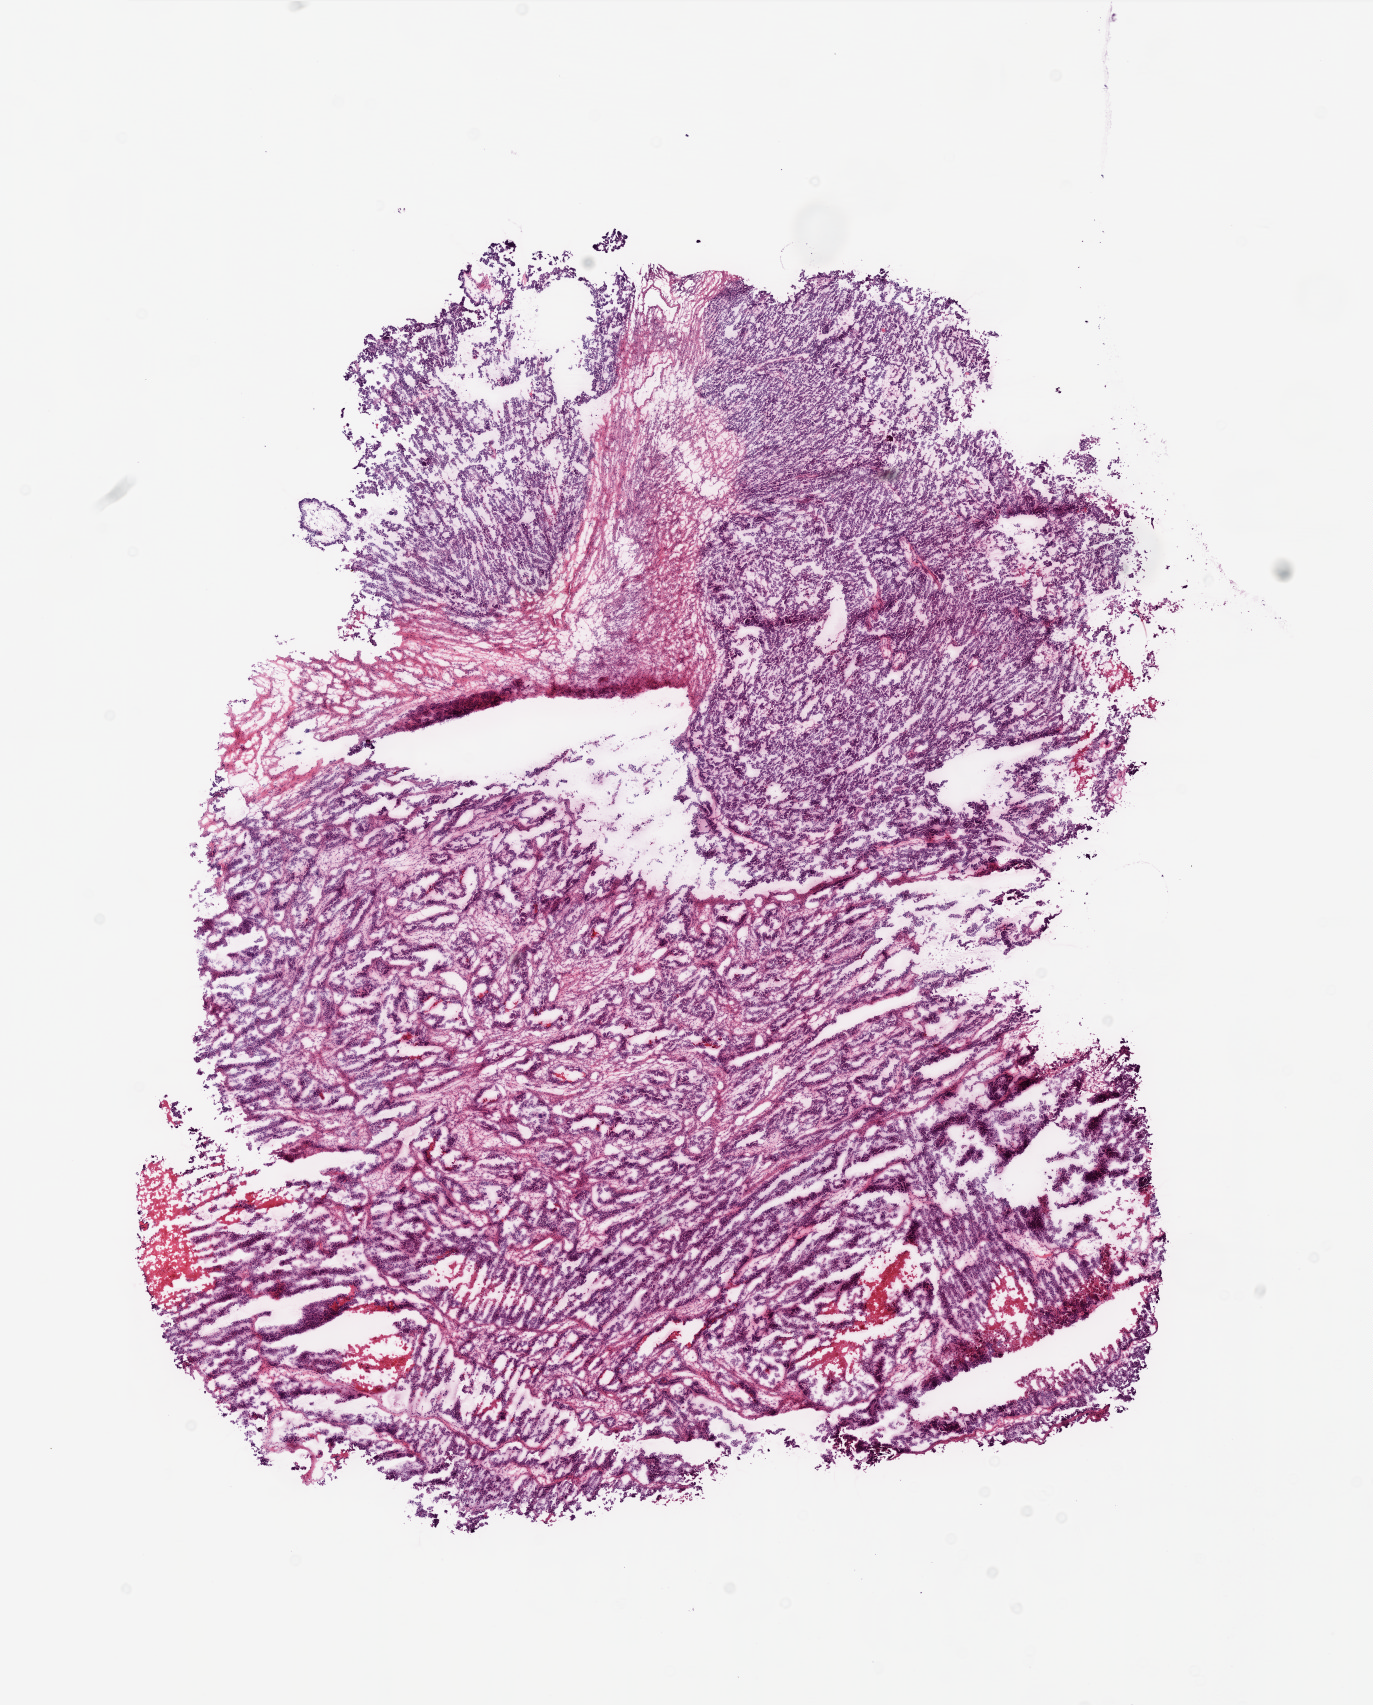
Hematoxylin and eosin (H&E) stained whole-slide image, shown as a low-resolution overview of the whole scanned area (about 11.0 x 13.6 mm, slide scanned at 20x), frozen section, sample: primary tumour, ovary. Patient: female, age at initial diagnosis 65 years. Histologic grade: G3 (poorly differentiated). Slide review estimates, as recorded: tumour cells 80%, tumour nuclei 90%, normal cells 0%, stromal cells 20%, necrosis 0%.
• pathologic diagnosis: Serous cystadenocarcinoma, NOS
• laterality: bilateral
• FIGO stage: IIIC